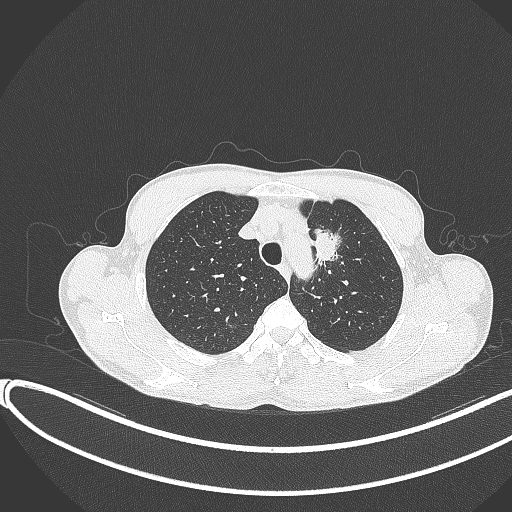
Chest CT, one axial slice; slice 308 of 374 in the series (ordered by position); reconstruction kernel B70f; 120 kVp; lung window (W 1500 / L -600 HU); 1 mm slice thickness; 512 × 512 image matrix, field of view 400 × 400 mm. Patient: male, 58 years. From the clinical record (not read from this slice): clinical TNM (as recorded): T1c N1 M0.
Annotated regions visible in this slice (rectangle marked by the reading radiologist):
- lung tumour (recorded histology: adenocarcinoma): bounding box [x1, y1, x2, y2] px = [309, 224, 358, 285]